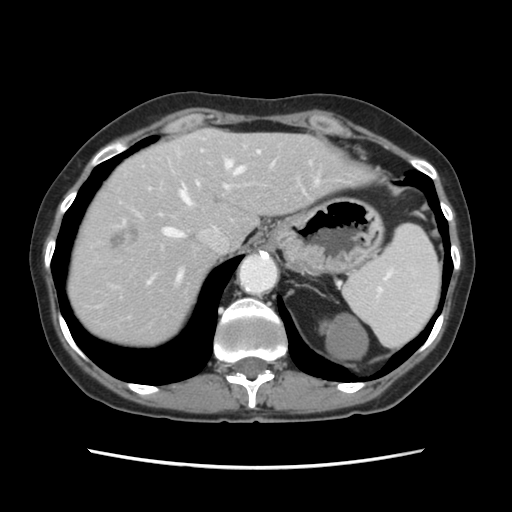
Contrast-enhanced abdominal CT, one axial slice. Slice 94 of 120 in the series (ordered by position). 120 kVp. Intravenous contrast given. Soft-tissue window (W 400 / L 40 HU). 2.5 mm slice thickness. 512 × 512 image matrix, field of view 330 × 330 mm. Female patient, age 70 years. From the clinical record (not read from this slice): diagnosis: colorectal cancer liver metastases, imaged before liver resection; multiple liver metastases: no; largest metastasis: 2.5 cm.
Annotated regions visible in this slice (manually delineated by an expert):
- hepatic veins: bounding box (x1, y1, x2, y2) in pixels: (163, 160, 244, 284)
- liver: (69, 130, 367, 347)
- planned liver remnant (the part of the liver to remain after resection): (135, 130, 365, 278)
- portal vein (with intrahepatic branches): (146, 150, 260, 285)
- liver metastasis: (111, 226, 140, 249)